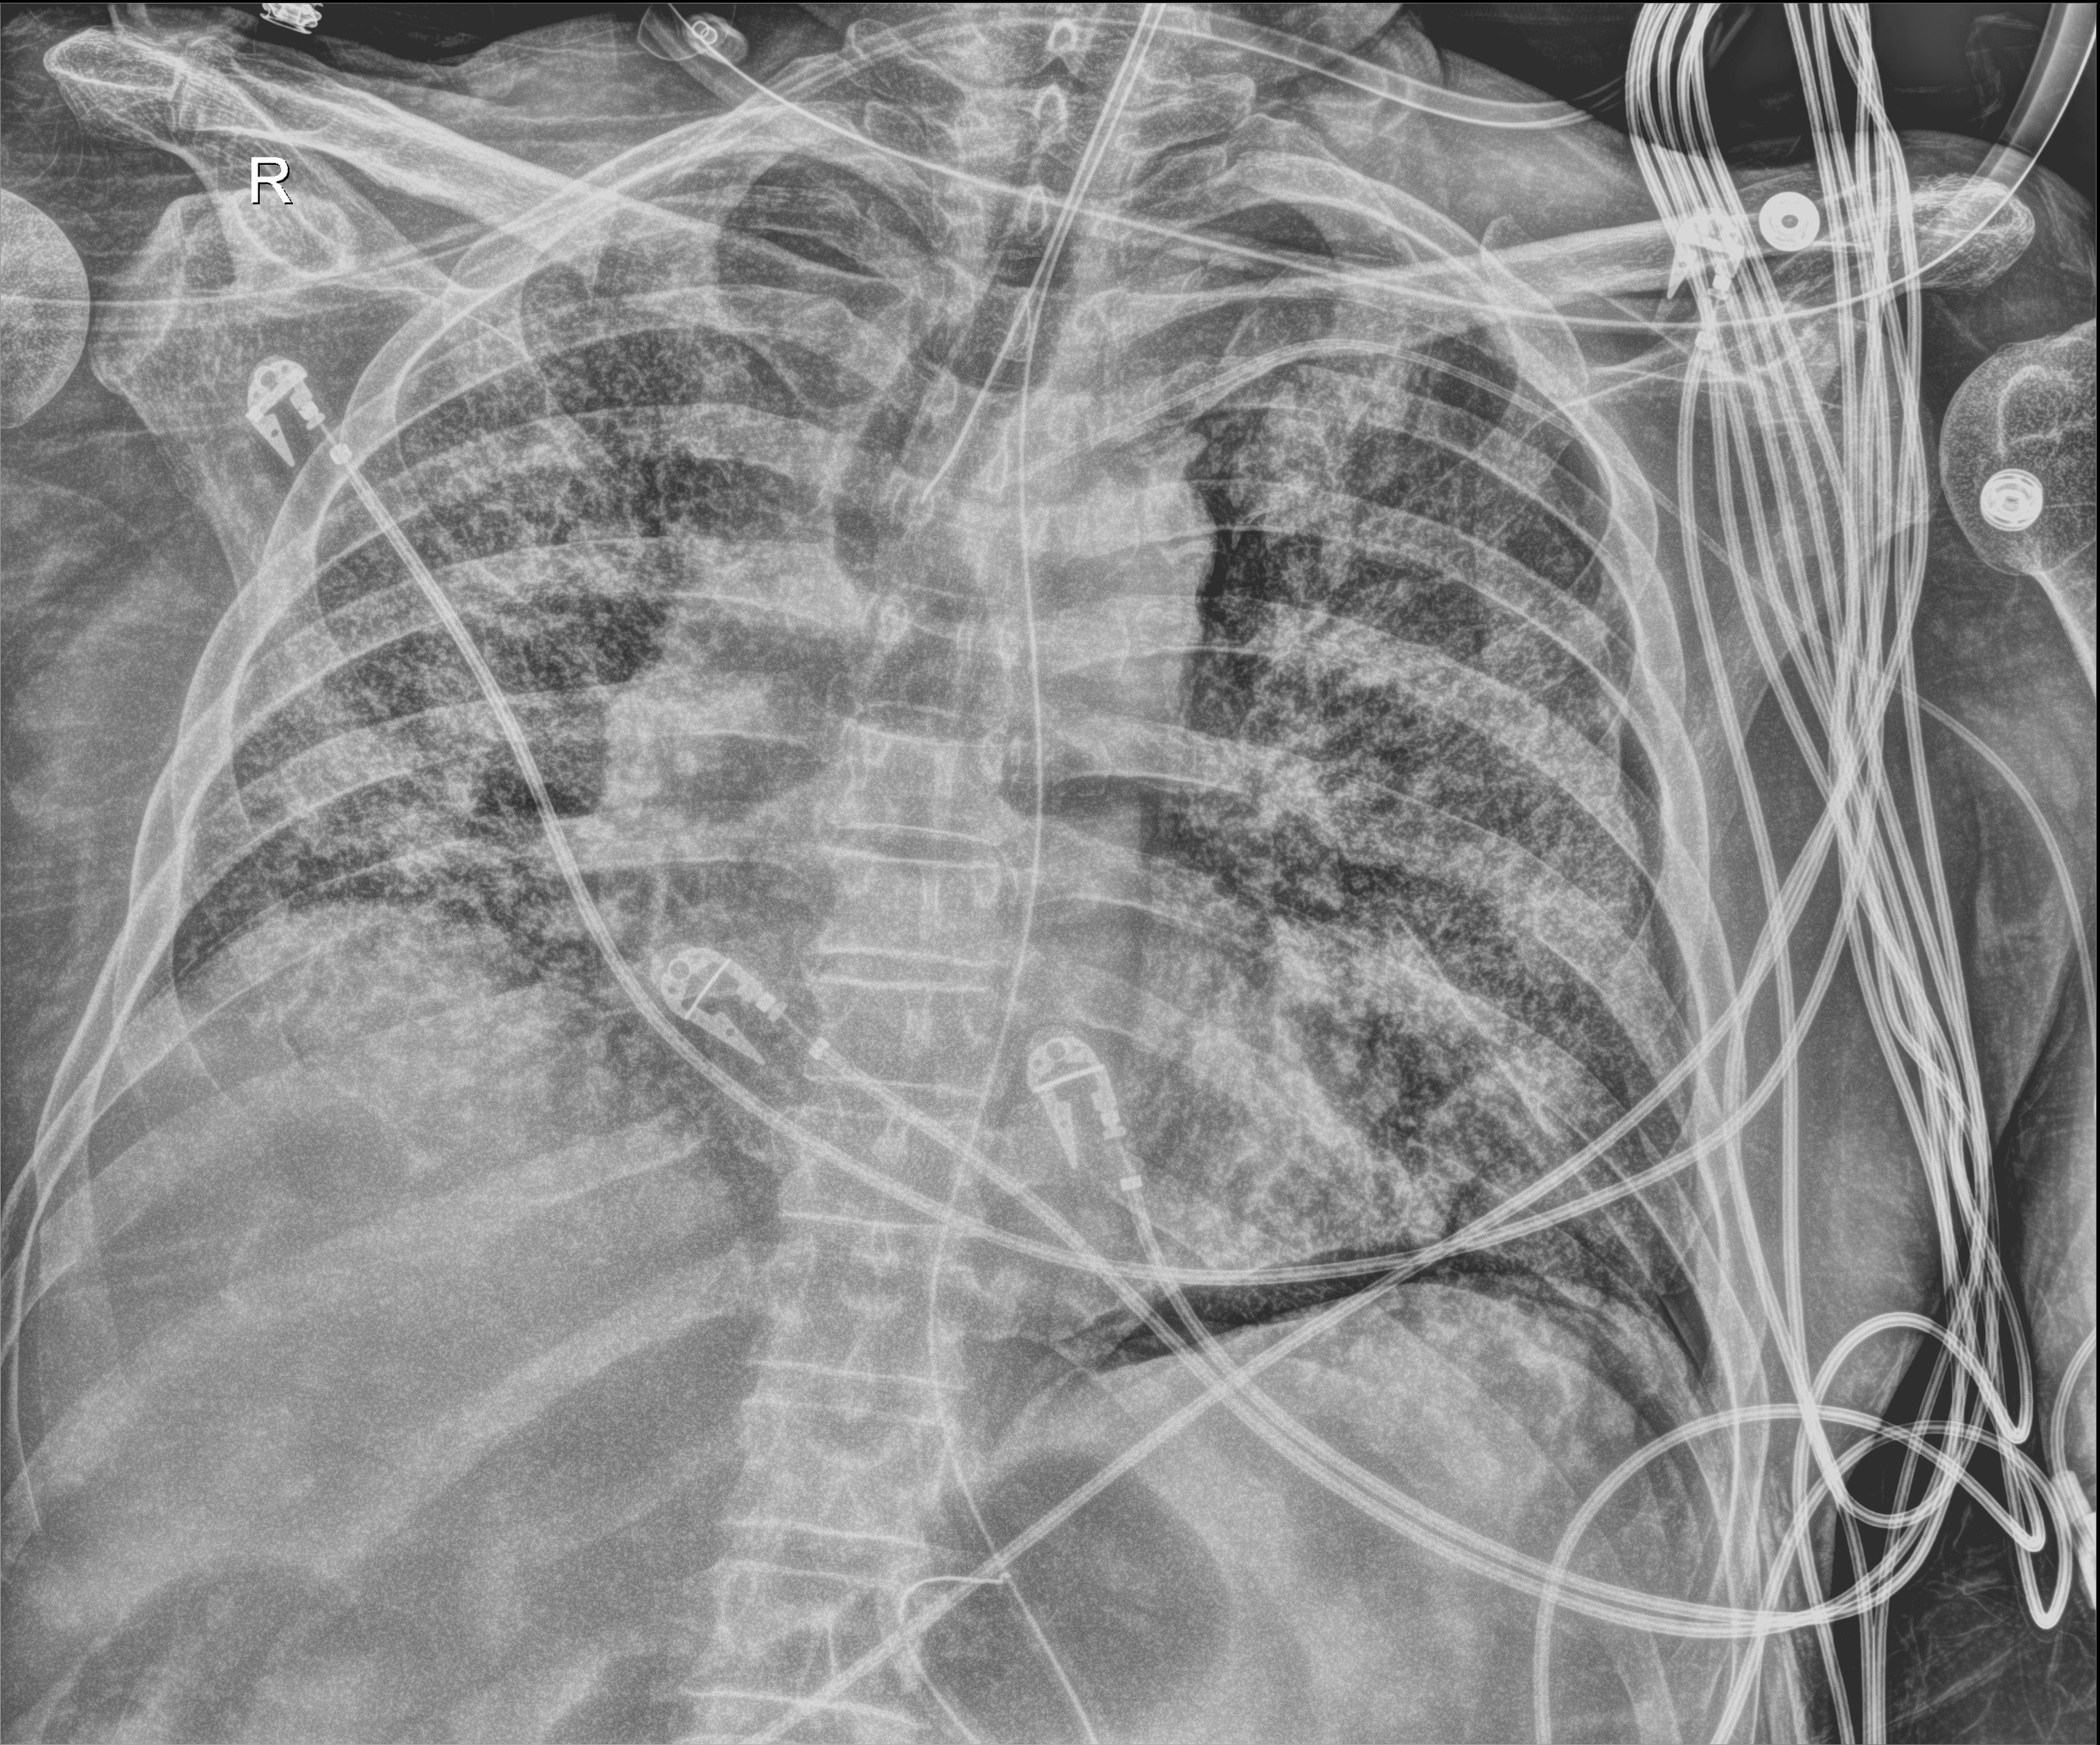
Chest radiograph (digital radiography), anteroposterior (AP) projection. Male patient hospitalised with COVID-19, age 60–74 years.
Admission-level facts for this patient (not findings on this image; timing relative to this image not recorded): admitted to intensive care during this hospital stay: yes.